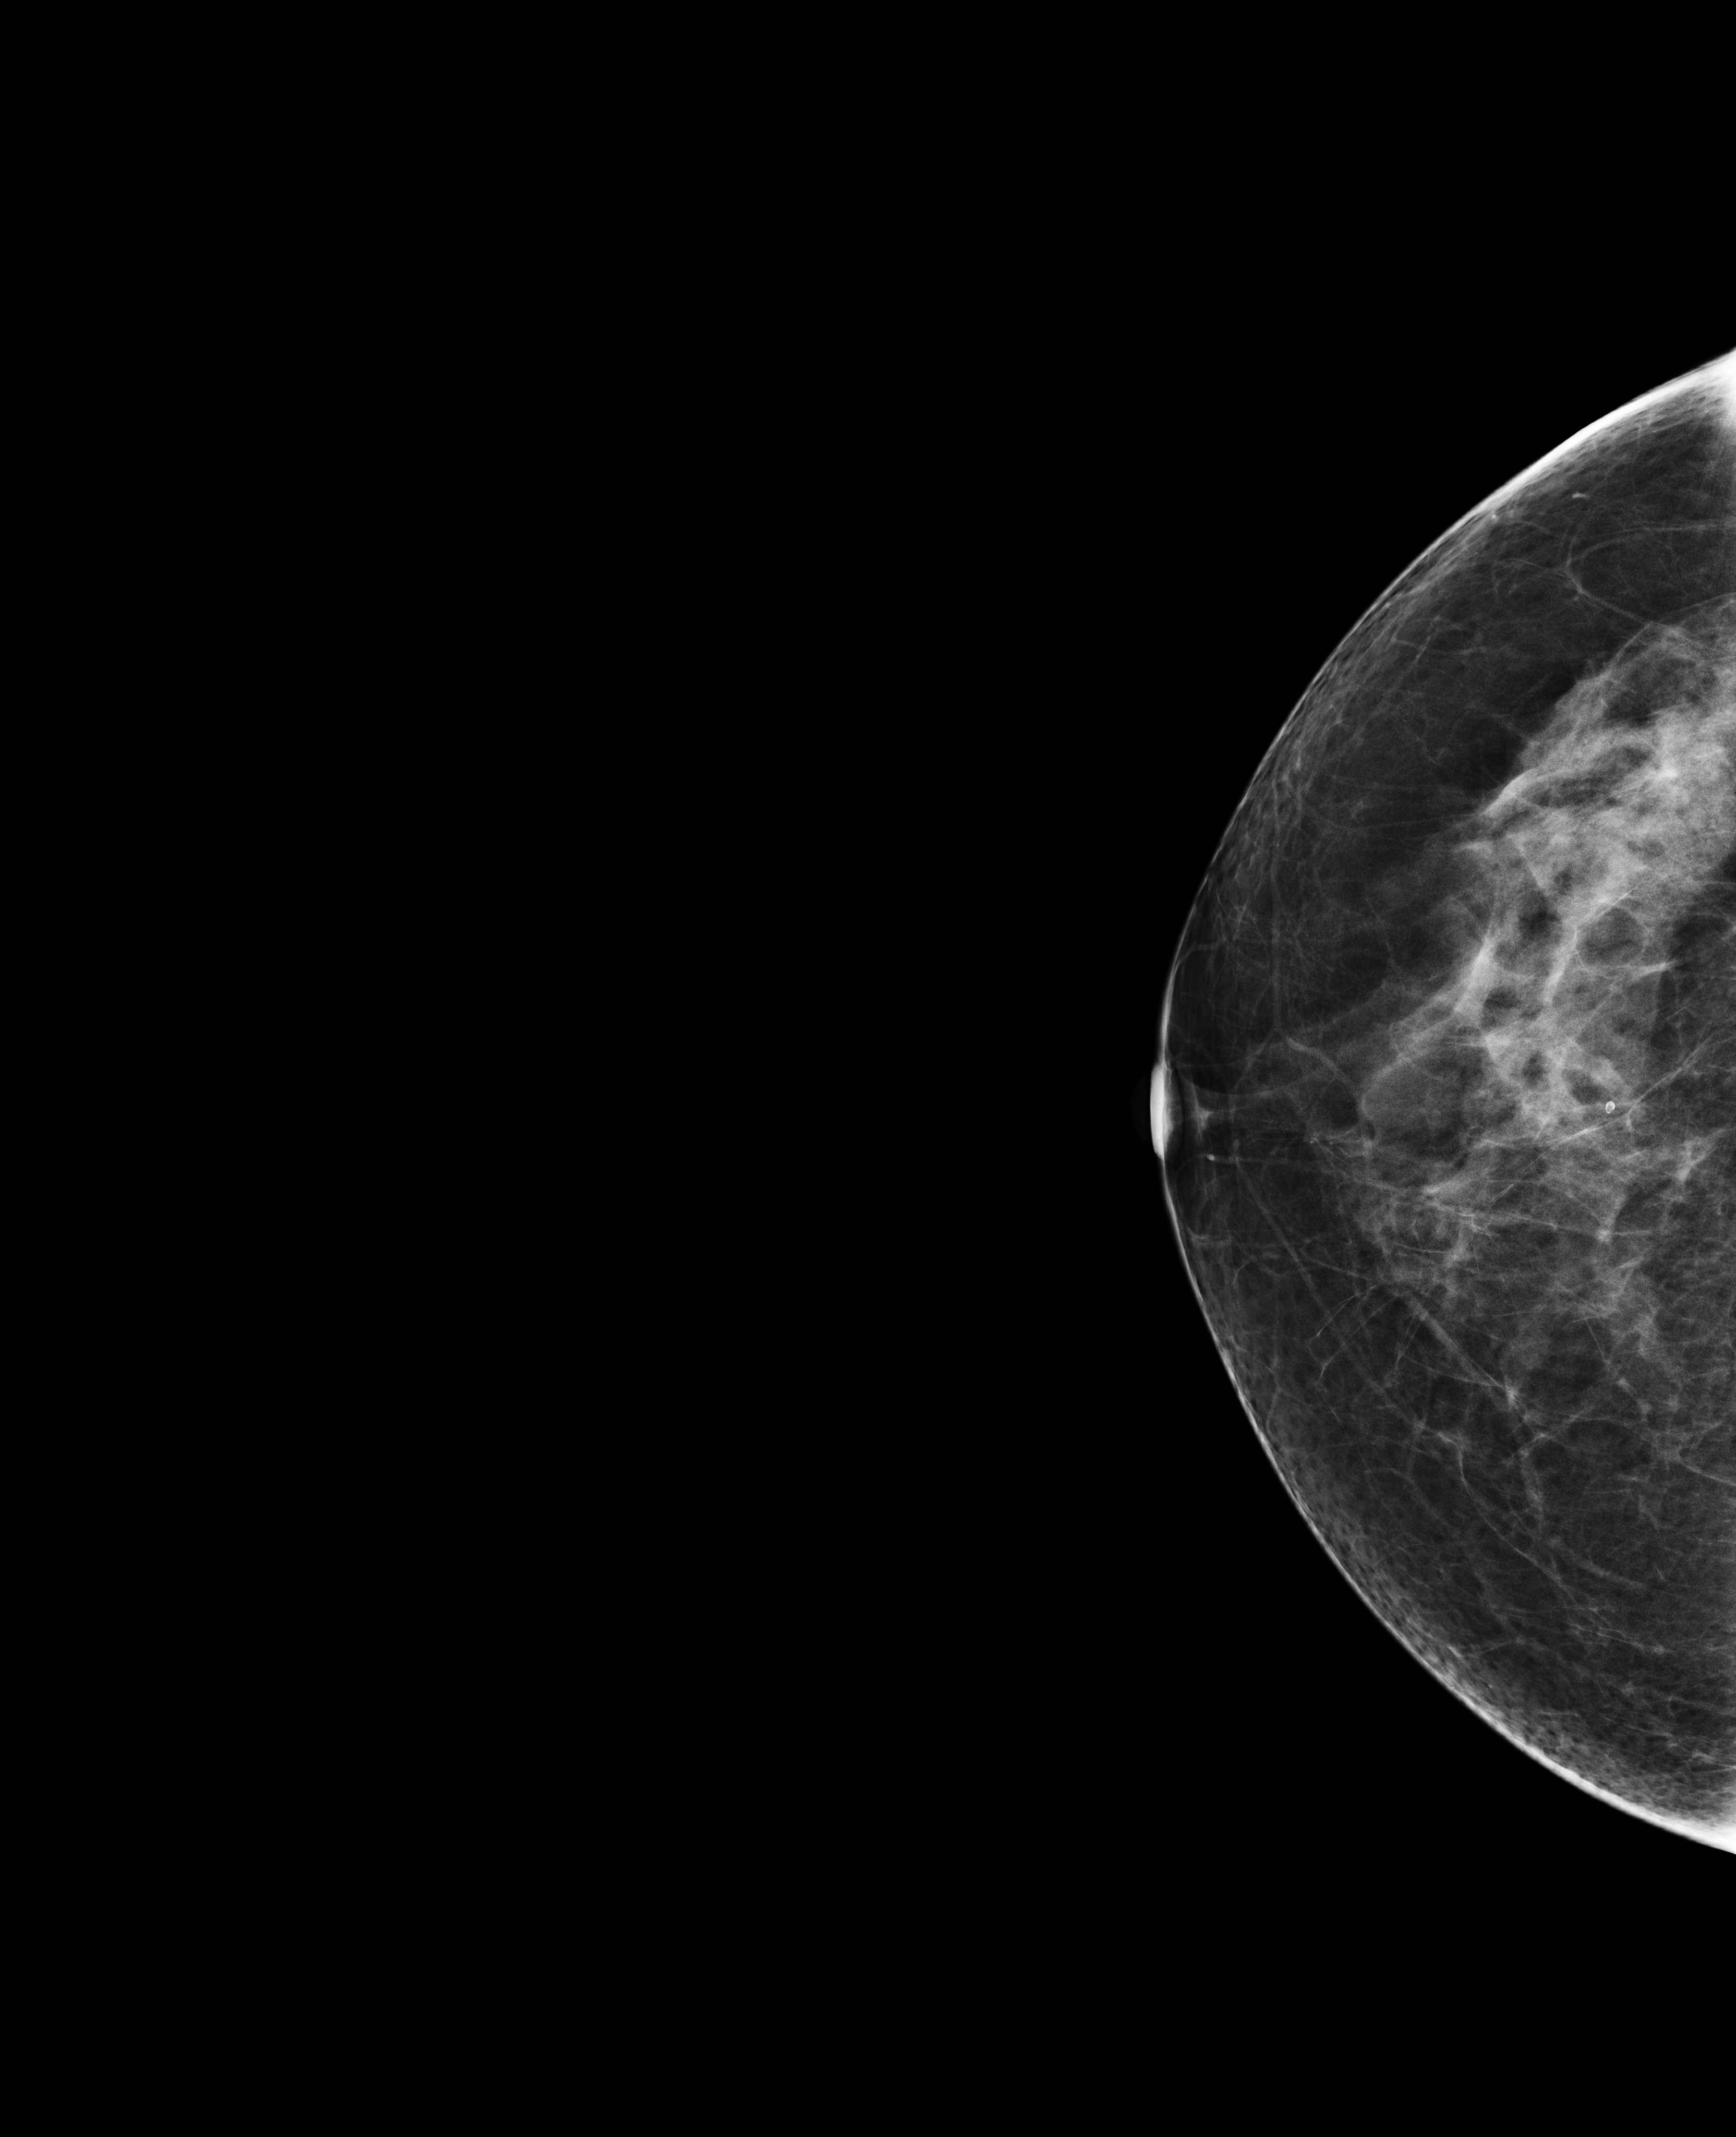
Annual screening mammography examination; system: Selenia Dimensions. Female patient, age 64 years.
Image type: full-field digital mammogram. Breast: right. Projection: CC view.